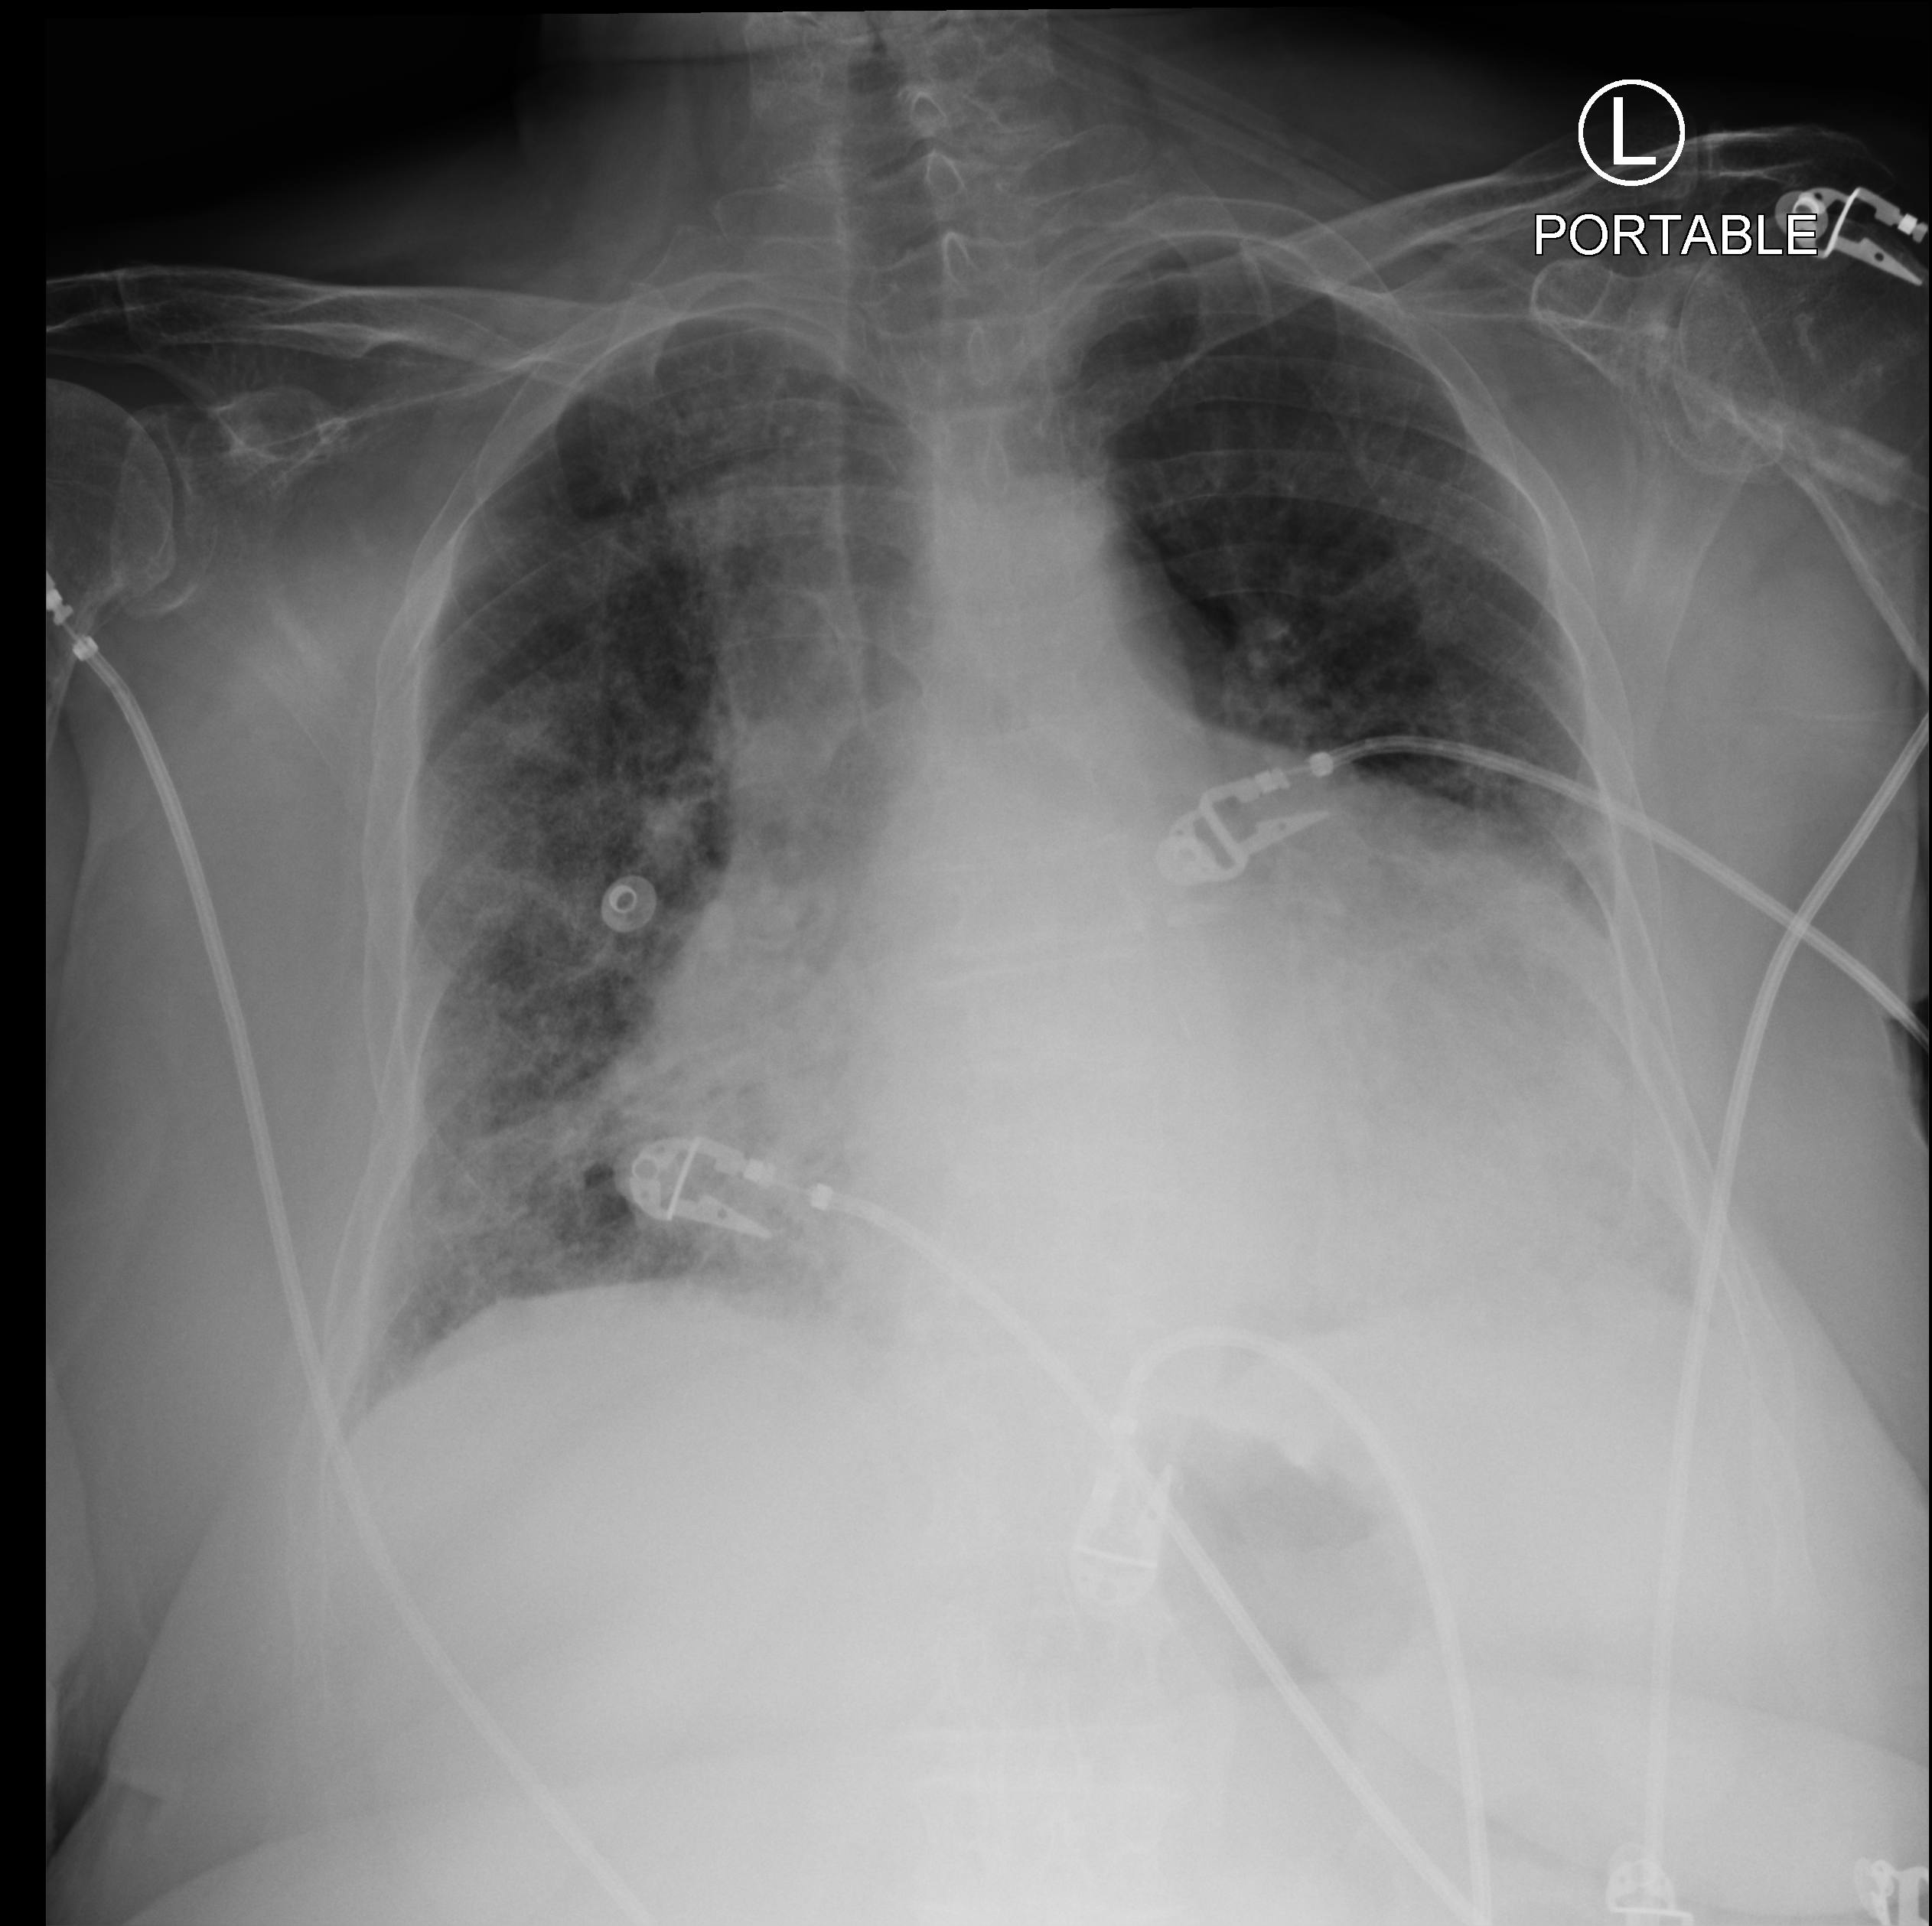
Chest X-ray (portable), anteroposterior (AP) projection. Female patient hospitalised with COVID-19, age 75–90 years.
Hospital-stay facts (about this admission, not read from this image; timing relative to this image not recorded): length of hospital stay: 10 days; mechanically ventilated during this hospital stay: no; admitted to intensive care during this hospital stay: no.